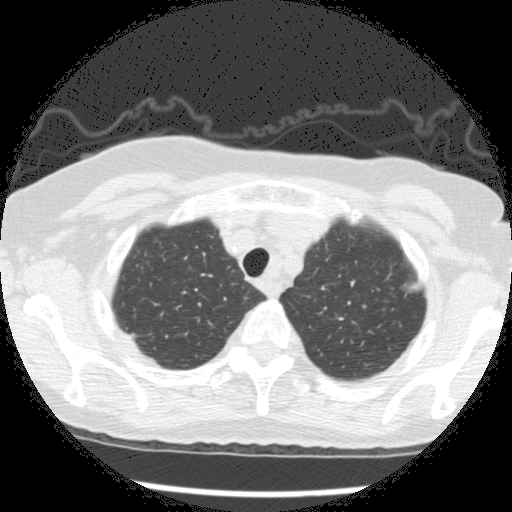
Low-dose screening chest CT, one axial slice; position 234 of 266 along the scan axis; reconstruction kernel STANDARD; 120 kVp; lung window (W 1500 / L -600 HU); 2.5 mm slice thickness; 512 × 512 image matrix, field of view 320 × 320 mm.
Structures marked on this image (outlined manually by an expert reader):
- lesion 1 (tumor, upper lobe of left lung): bounding box [x1, y1, x2, y2] px = [409, 282, 421, 291]